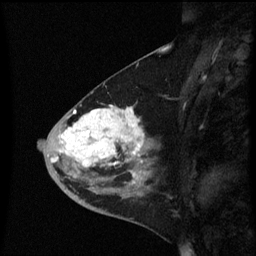
Breast MRI (dynamic contrast-enhanced), one sagittal slice. Slice 26 of 60 in the series (ordered by position). Dynamic contrast-enhanced series, image 2 of 3 at this slice position (ordered by acquisition). 1.5 T. TE 4.2 ms, TR 8.4 ms. 256 × 256 image matrix, field of view 200 × 200 mm. Patient: female, 46 years. From the clinical record (not read from this slice): setting: breast cancer imaged before/during neoadjuvant chemotherapy; receptor status: HER2-positive.
Structures marked on this image (semi-automatically segmented with operator editing):
- analysis volume of interest (the breast-tissue region the enhancement analysis was run in; not a lesion): bounding box <38,96,160,187> (left, top, right, bottom; pixels)
- tumour enhancement mask (voxels above the 70 % enhancement threshold inside the analysis volume of interest): <51,106,145,185>